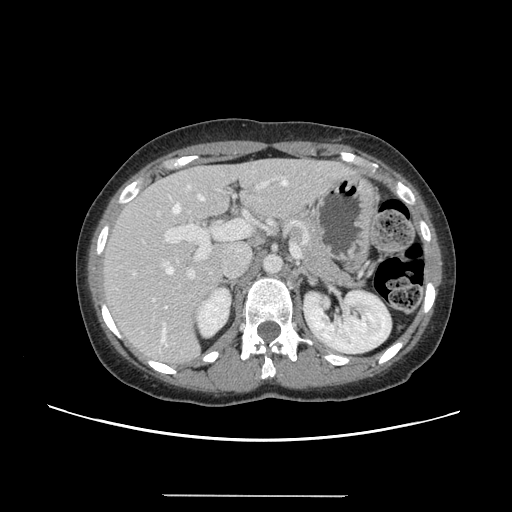
Contrast-enhanced abdominal CT, one axial slice; position 85 of 144 along the scan axis; 120 kVp; soft-tissue window (W 400 / L 40 HU); 2.5 mm slice thickness; 512 × 512 image matrix, field of view 380 × 380 mm. Female patient, age 53 years. Case-level facts recorded for this patient, not image findings: diagnosis: colorectal cancer liver metastases, imaged before liver resection; multiple liver metastases: yes; largest metastasis: 1.1 cm; disease in both lobes: no.
Structures marked on this image (expert manual segmentation):
- hepatic veins: bounding box <162,180,288,343> (left, top, right, bottom; pixels)
- liver: <105,160,351,363>
- planned liver remnant (the part of the liver to remain after resection): <106,159,315,297>
- portal vein (with intrahepatic branches): <133,179,300,302>